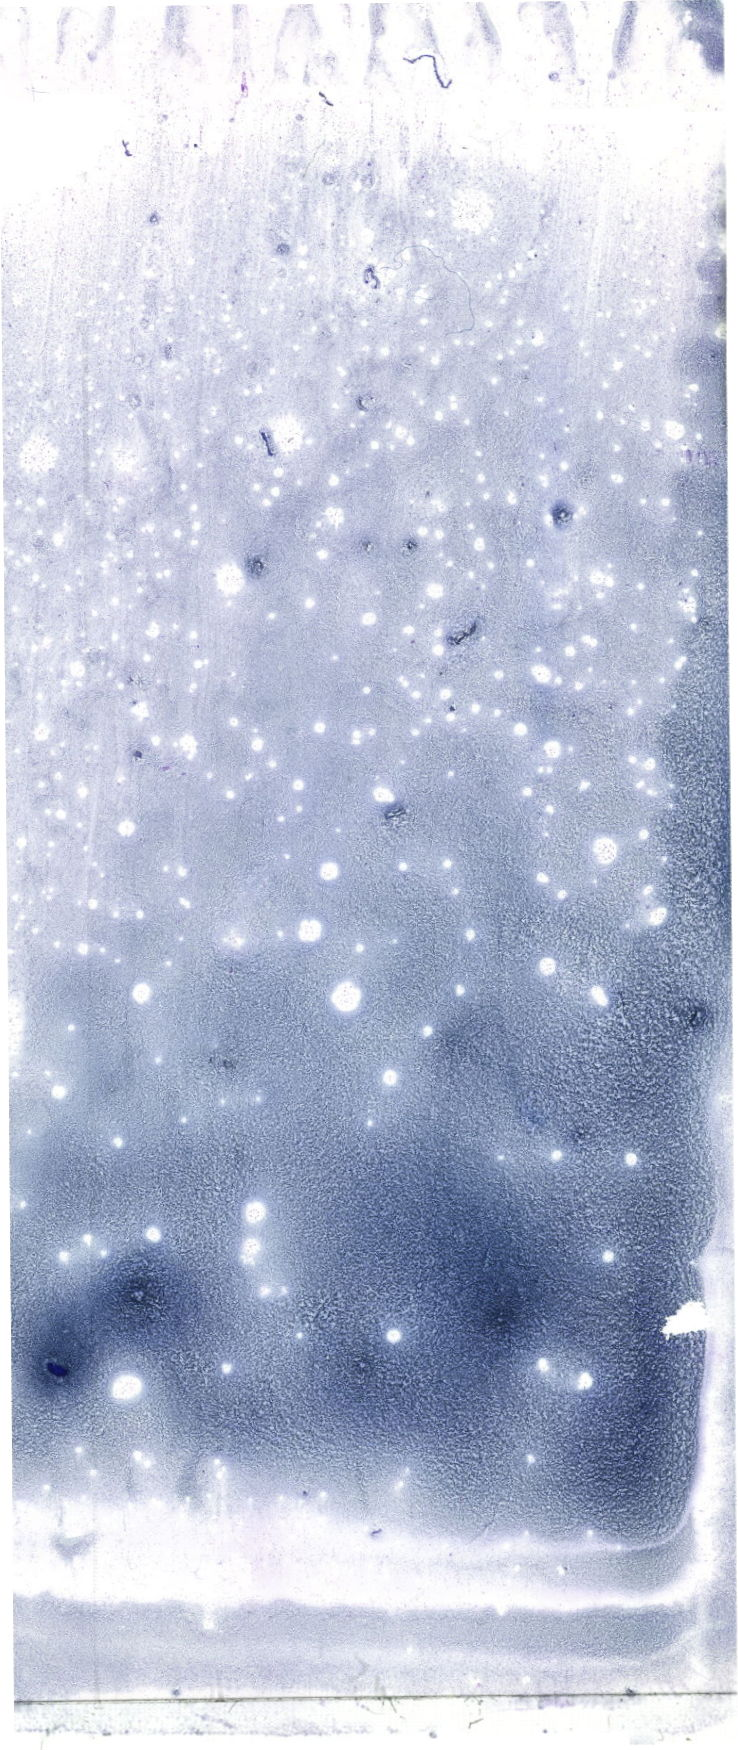
Bone marrow aspirate smear, May-Grünwald-Giemsa (MGG) stain, whole-slide image — shown as a low-resolution overview of the whole scanned area (about 20.9 x 49.6 mm). Patient sex: female.
Diagnosis: B Acute Lymphoblastic Leukemia.